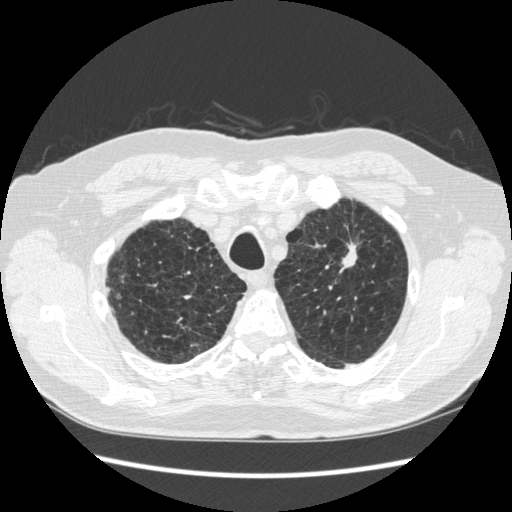
Low-dose screening chest CT, one axial slice. Slice 225 of 267 in the series (ordered by position). Reconstruction kernel STANDARD. 120 kVp. Lung window (W 1500 / L -600 HU). 512 × 512 image matrix.
Outlined on this slice (outlined manually by an expert reader):
- lesion 1 (tumor, upper lobe of left lung): bounding box (x1, y1, x2, y2) in pixels: (340, 242, 357, 273)